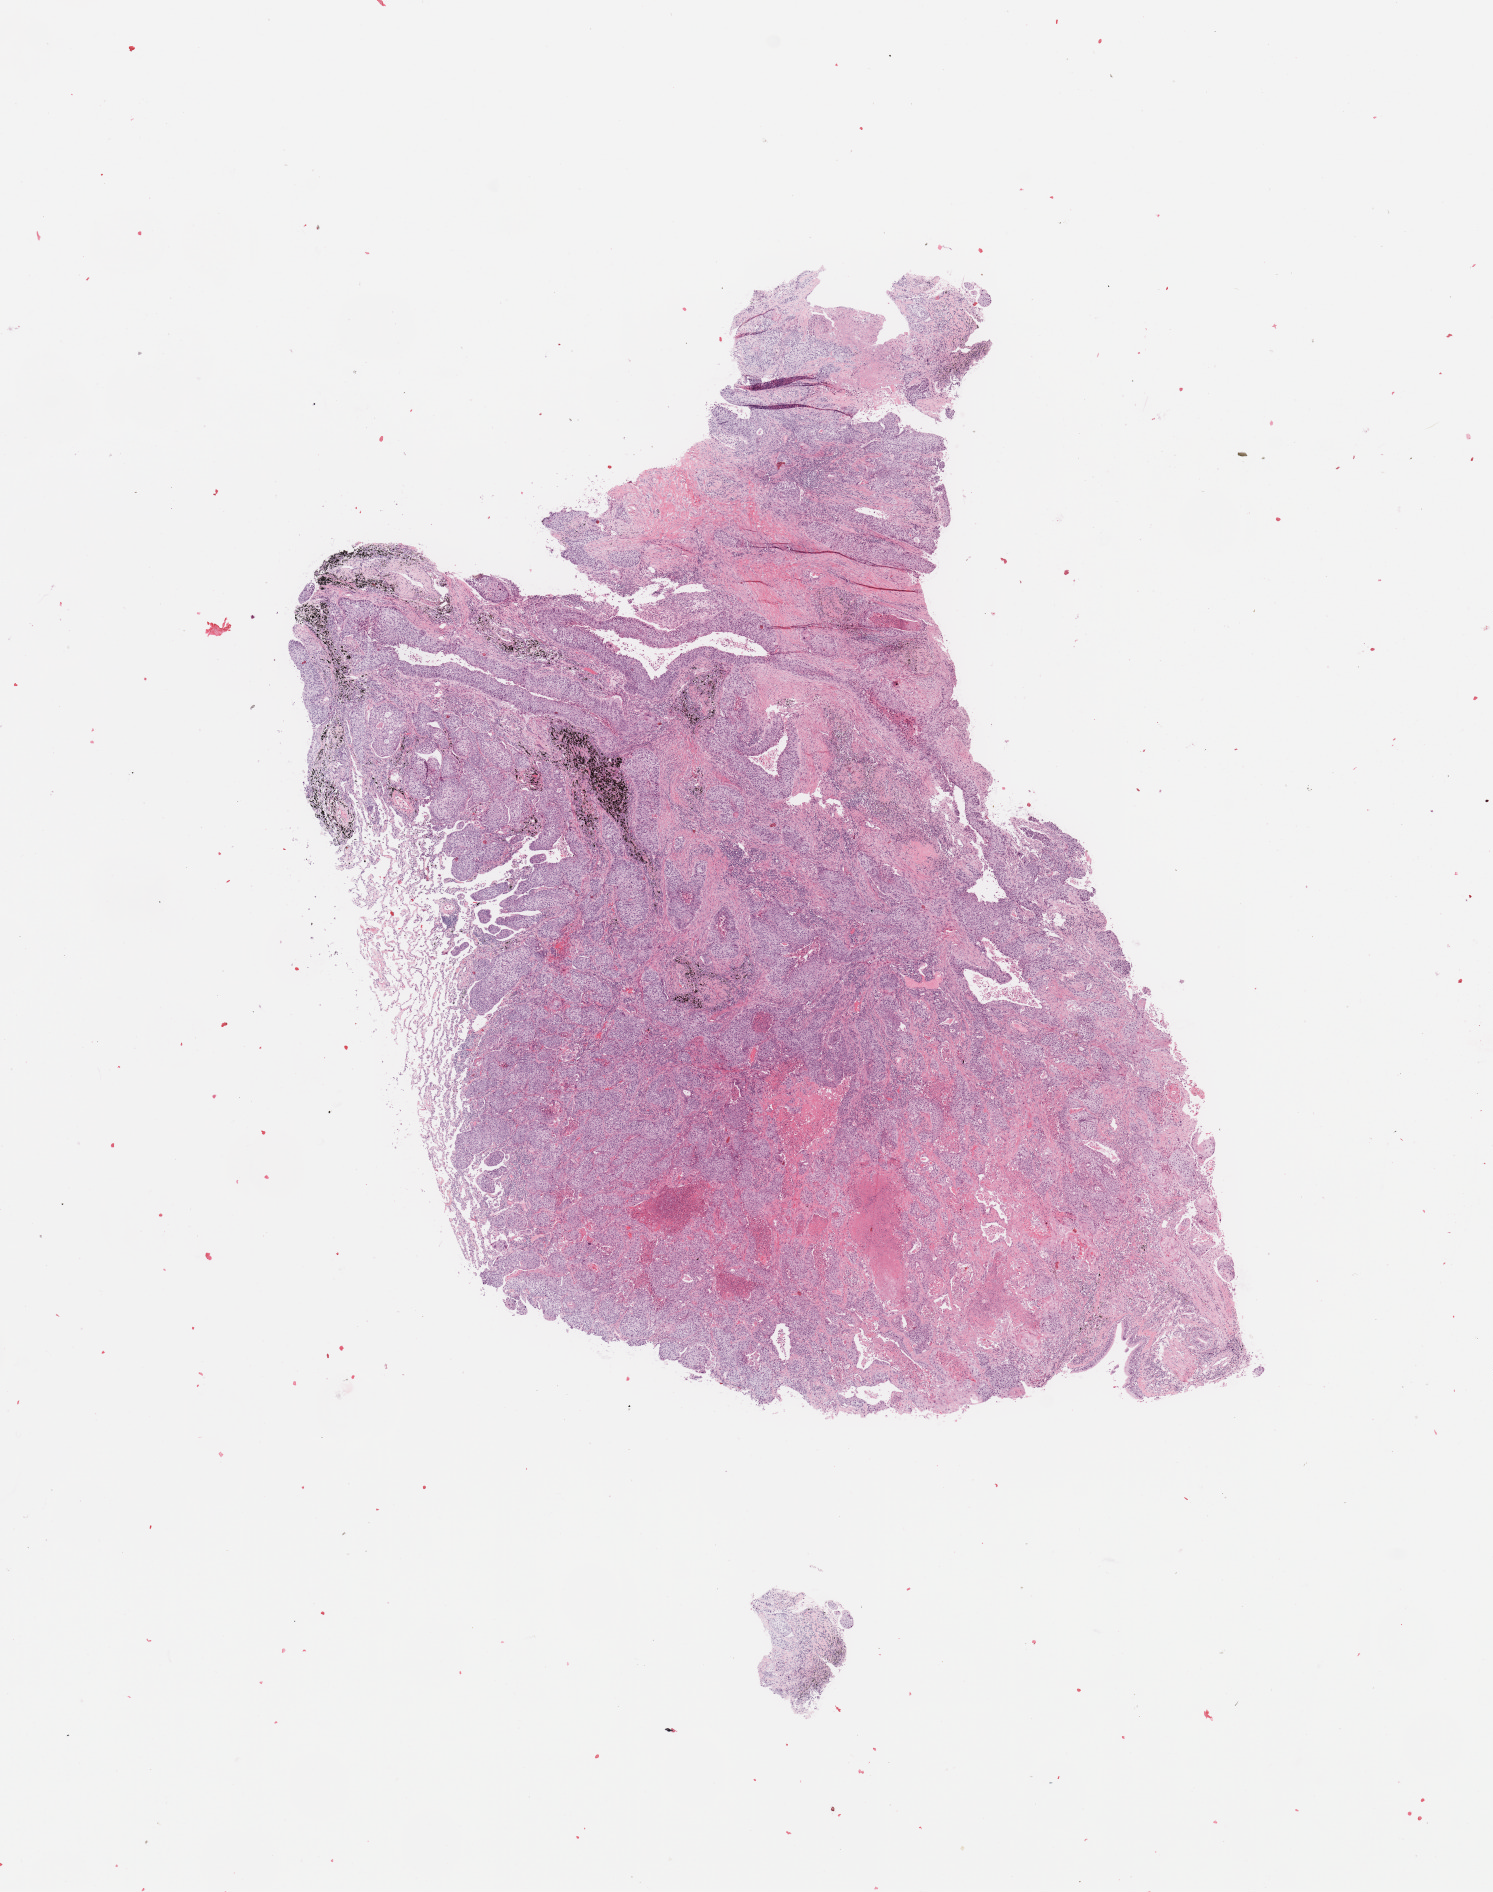
H&E-stained whole-slide image, a low-resolution overview of the entire scanned area, about 11.8 x 15.0 mm; tumour tissue sample, lung. Patient: male, age 65 years. Histologic grade: G3 (poorly differentiated).
• AJCC pathologic stage: IIIA
• primary tumour site (as recorded): right upper lobe
• diagnosis: Squamous cell carcinoma, NOS